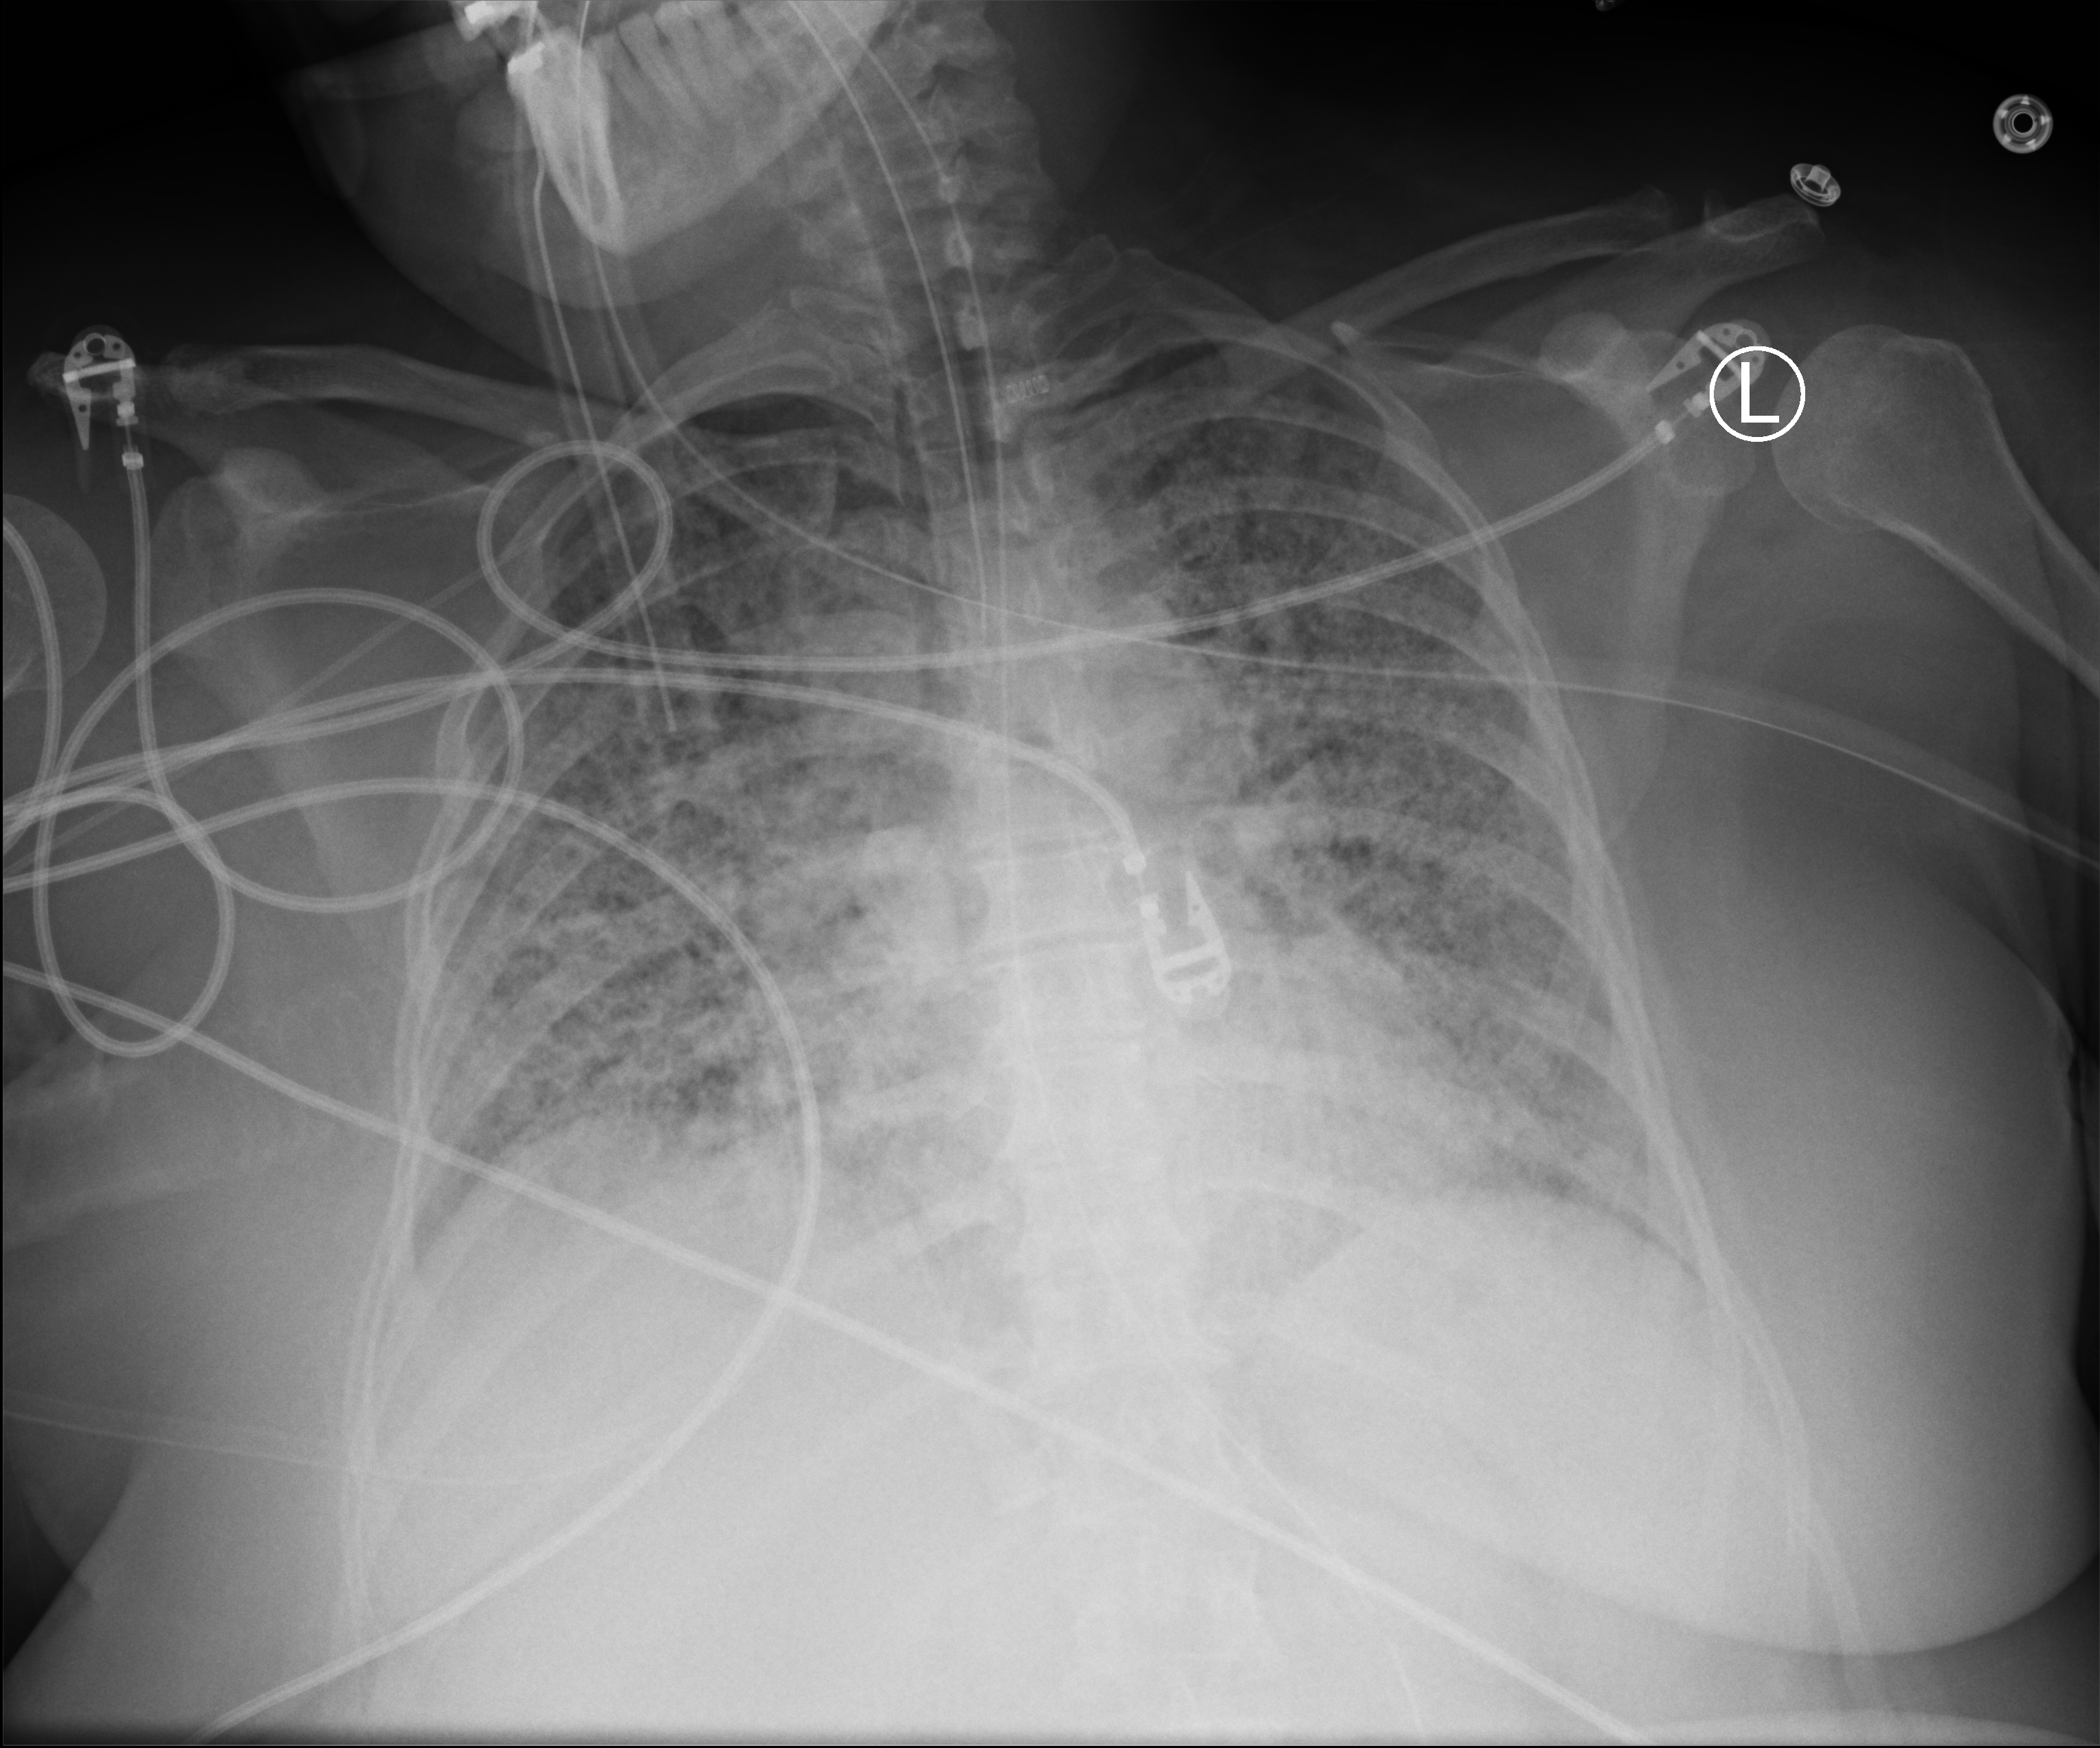
Chest X-ray (portable), anteroposterior (AP) projection. Patient hospitalised with COVID-19; female, aged 18–59 years.
Admission-level facts for this patient (not findings on this image; timing relative to this image not recorded): hypertension (admission record): yes; COPD (admission record): no; length of hospital stay: 95 days.